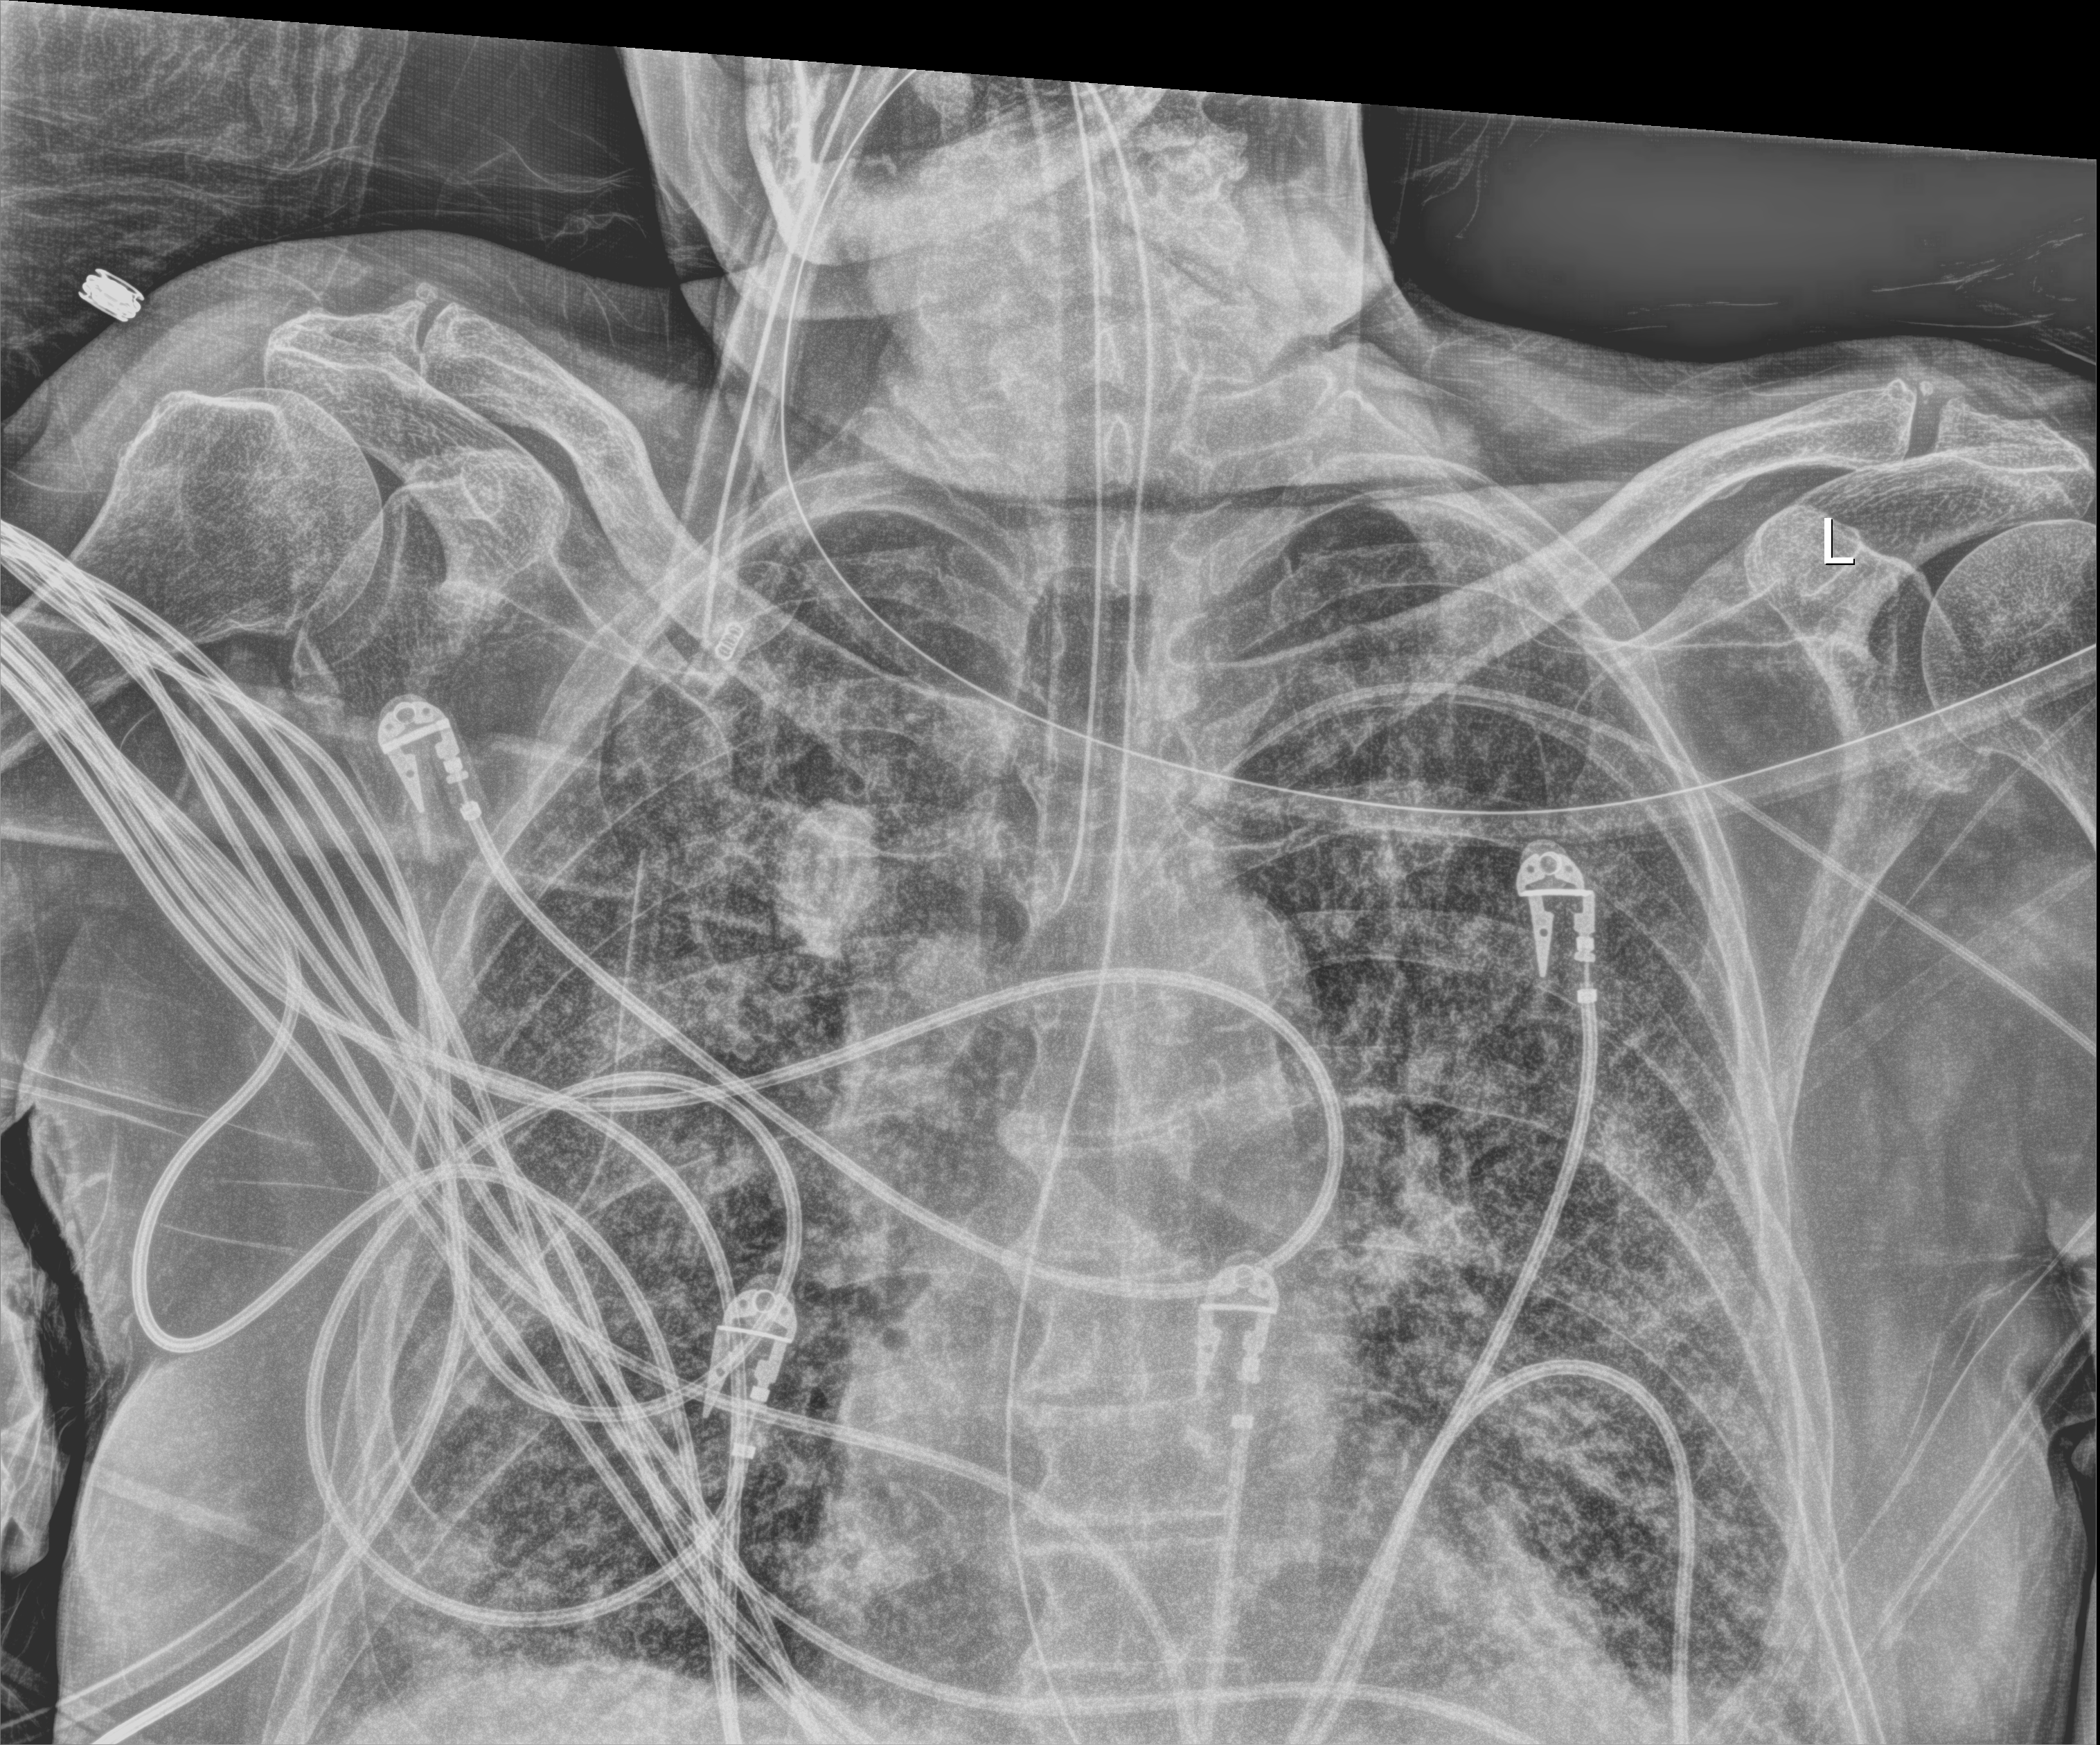
Chest X-ray (portable); anteroposterior (AP) projection. Male patient hospitalised with COVID-19, age 75–90 years.
From the hospital-stay record, not from the radiograph (when in the stay this image was taken is not recorded):
- admitted to intensive care during this hospital stay: yes
- mechanically ventilated during this hospital stay: yes